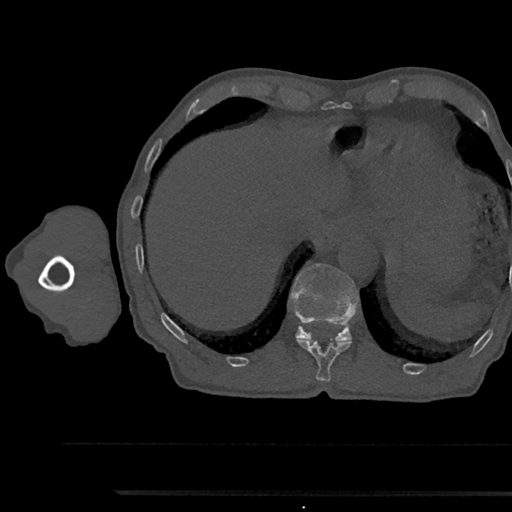
CT including the spine, one axial slice. Position 754 of 797 along the scan axis. 120 kVp. Bone window (W 1800 / L 400 HU). 0.5 mm slice thickness. 512 × 512 image matrix. Male patient, age 79 years. From the clinical record (not read from this slice): primary cancer: prostate.
Annotated regions visible in this slice (semi-automatic segmentation, software-assisted and operator-edited):
- T11 vertebra: box from (x=298, y=339) to (x=351, y=382) px
- T12 vertebra: (x=290, y=264)–(x=359, y=342)